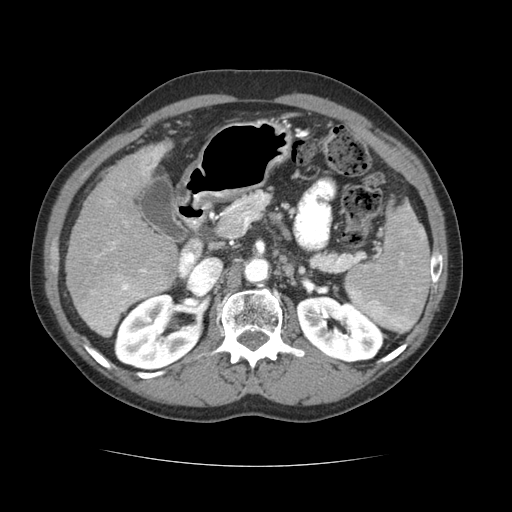
Contrast-enhanced abdominal CT (liver protocol), one axial slice; slice 35 of 69 in the series (ordered by position); reconstruction kernel STANDARD; 120 kVp; soft-tissue window (W 400 / L 40 HU); 512 × 512 image matrix. Case-level facts recorded for this patient, not image findings: diagnosis: hepatocellular carcinoma (patient treated with transarterial chemoembolisation; whether this scan precedes or follows treatment is not stated here); TNM stage (as recorded): Stage-II; Child-Pugh class: B; tumour differentiation: poorly differentiated; tumour nodularity: multinodular.
Annotated regions visible in this slice (semi-automatic segmentation, software-assisted and operator-edited):
- liver parenchyma outside the tumour (the mass and vessels are separate outlines, so this box may not span the whole liver): bounding box <64,142,178,336> (left, top, right, bottom; pixels)
- mass: <76,266,171,335>
- liver vessels: <98,147,164,257>